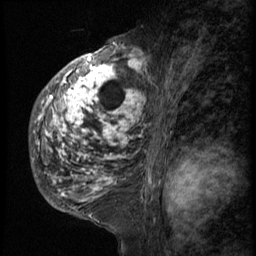
Breast MRI (dynamic contrast-enhanced), one sagittal slice. Position 34 of 58 along the scan axis. 3 images stored at this slice position (order not interpretable as contrast timing). 1.5 T. TE 4.2 ms, TR 9 ms. 2.5 mm slice thickness. 256 × 256 image matrix, field of view 180 × 180 mm. Female patient, age 50 years. From the clinical record (not read from this slice): setting: breast cancer imaged before/during neoadjuvant chemotherapy; receptor status: triple-negative.
Outlined on this slice (semi-automatically segmented with operator editing):
- analysis volume of interest (the breast-tissue region the enhancement analysis was run in; not a lesion): bounding box [x1, y1, x2, y2] px = [30, 48, 144, 214]
- tumour enhancement mask (voxels above the 140 % enhancement threshold inside the analysis volume of interest): [34, 48, 144, 202]